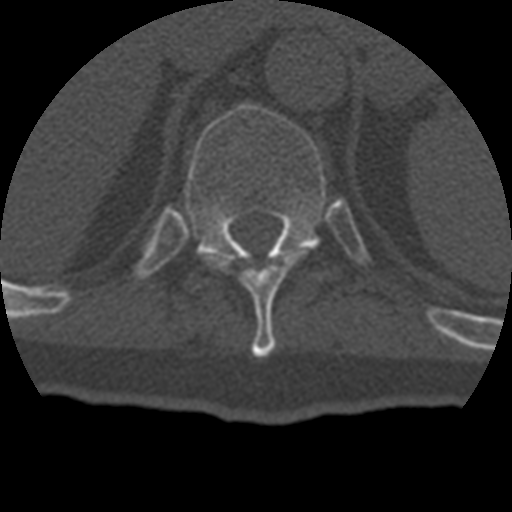
CT including the spine, one axial slice; position 206 of 399 along the scan axis; reconstruction kernel STANDARD; 120 kVp; bone window (W 1800 / L 400 HU); 512 × 512 image matrix. Patient age 69 years. Case-level facts recorded for this patient, not image findings: primary cancer: prostate.
Outlined on this slice (semi-automatically segmented with operator editing):
- T10 vertebra: bounding box <210,254,298,357> (left, top, right, bottom; pixels)
- T11 vertebra: <185,103,327,260>